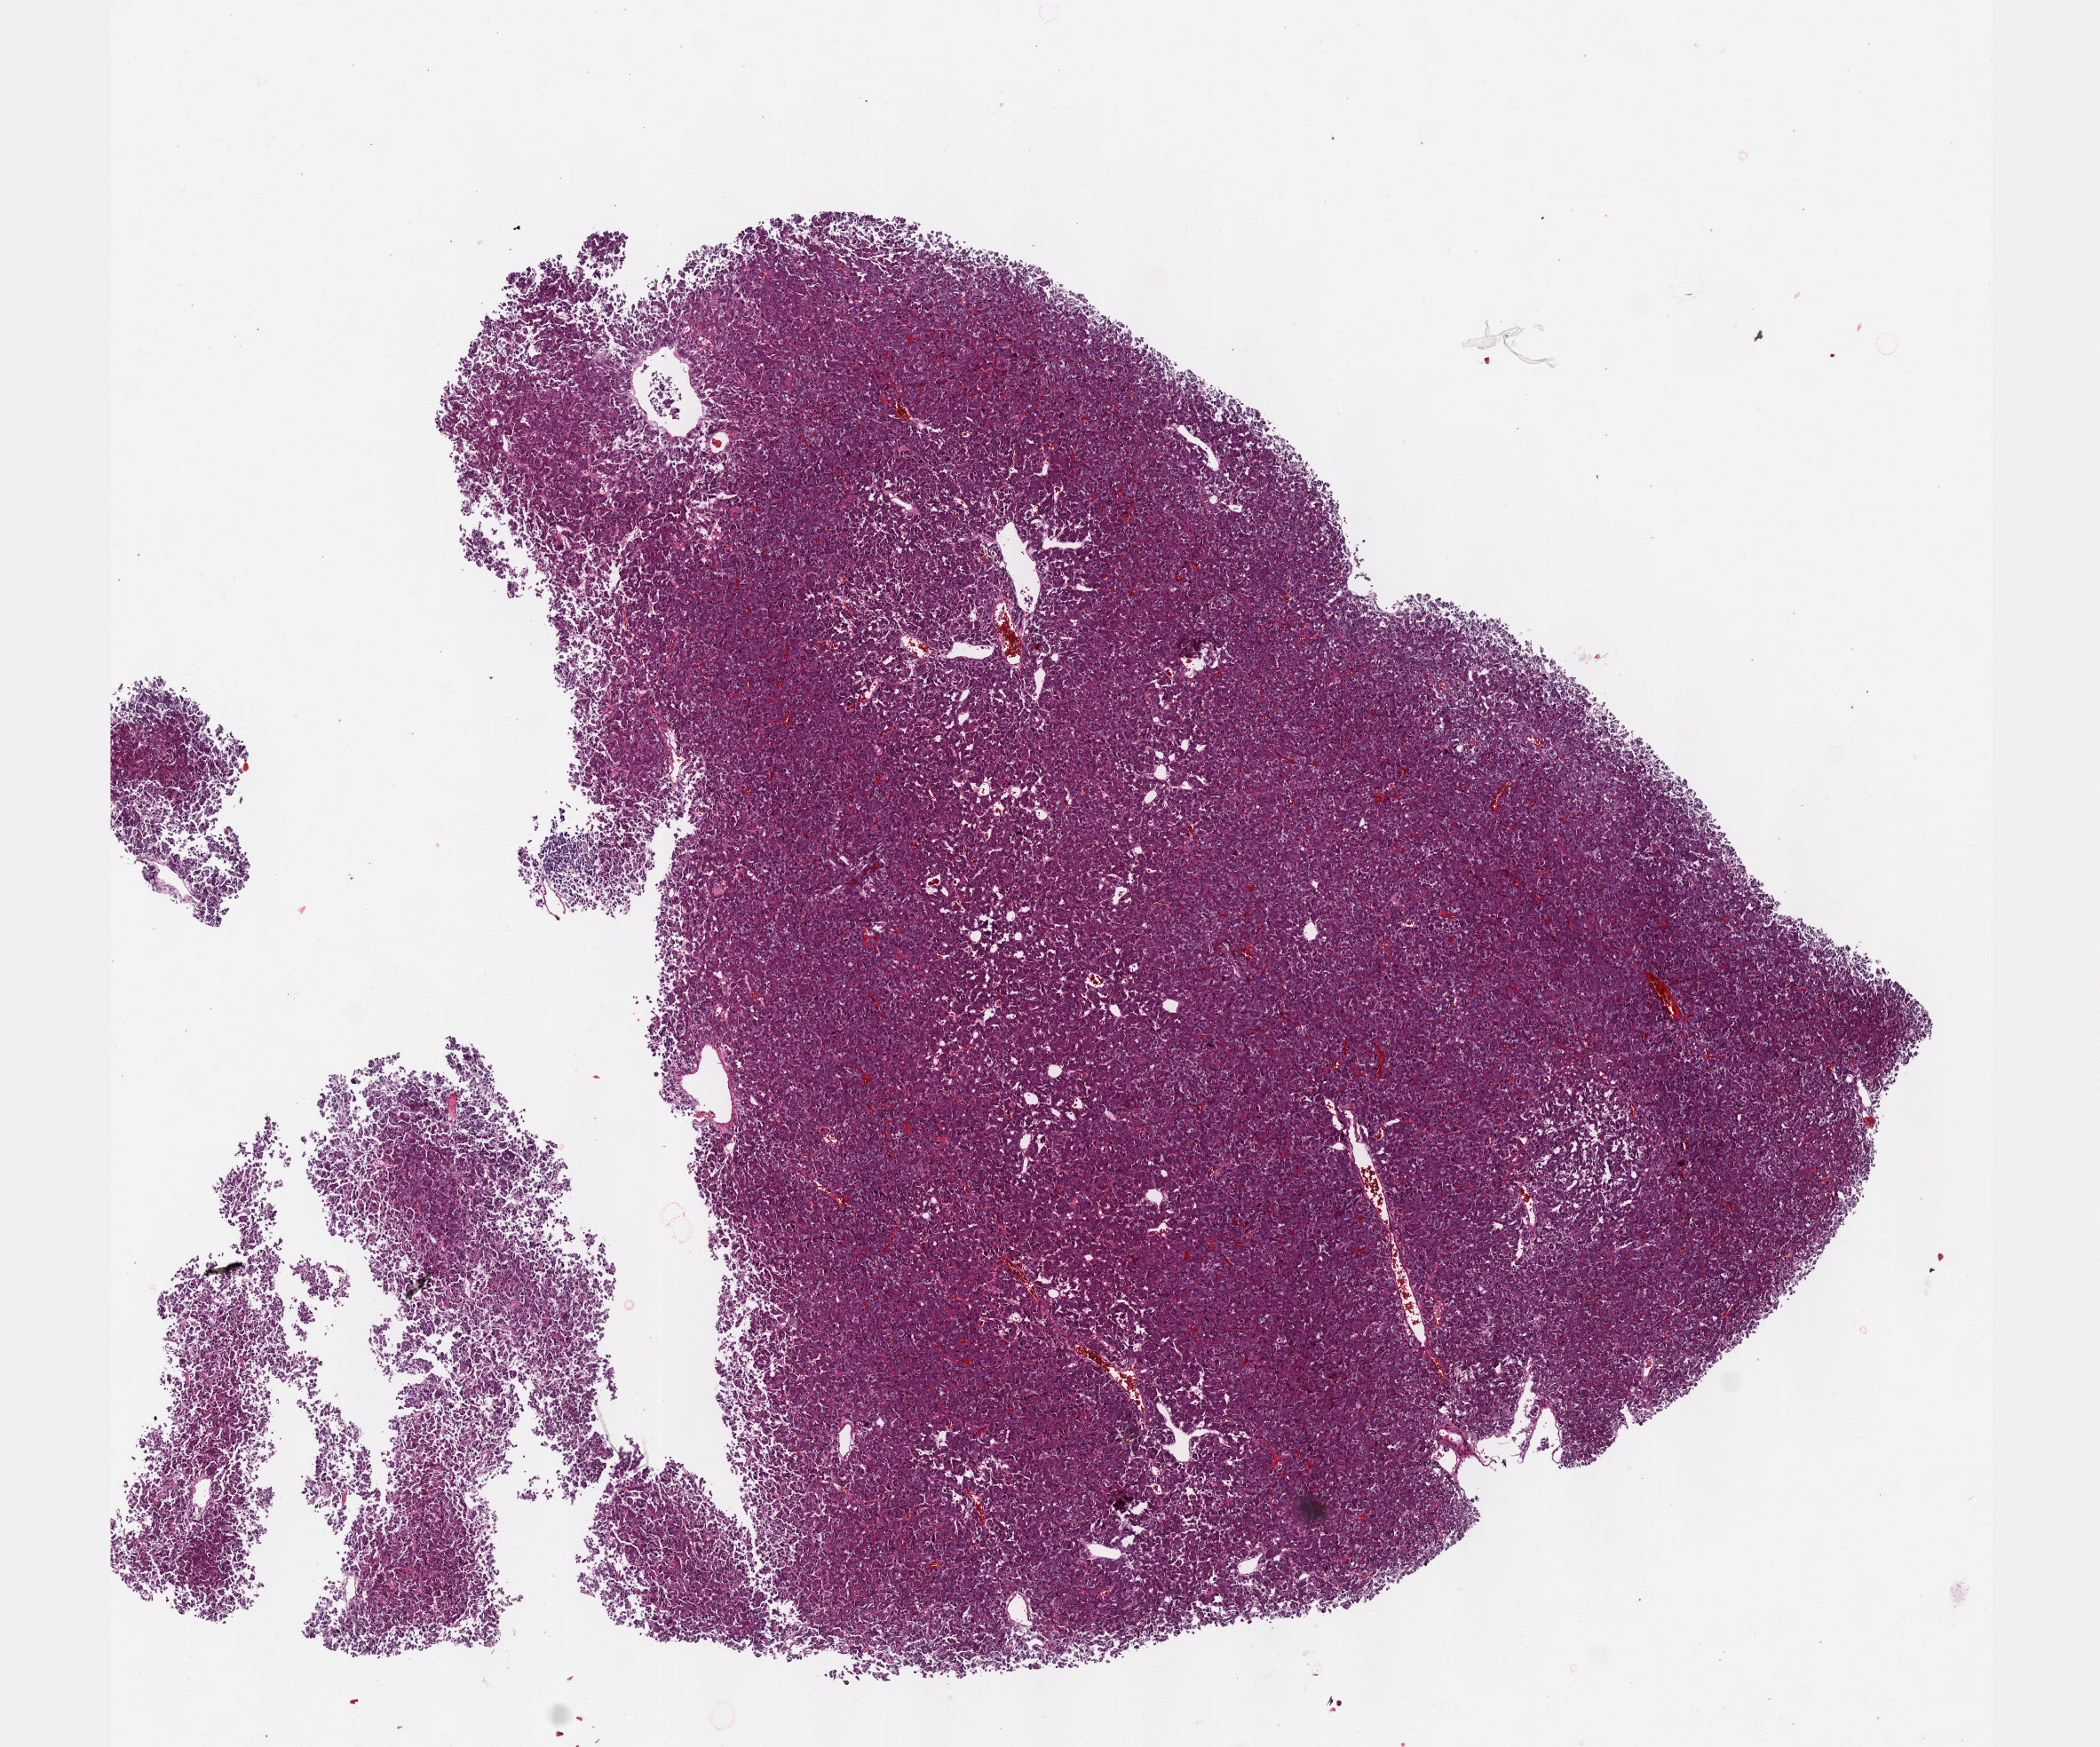
Whole-slide histology image, H&E-stained, low-resolution overview of the scanned area, about 9.6 x 8.0 mm. Formalin-fixed paraffin-embedded (FFPE) diagnostic section. Primary tumour sample from the adrenal gland. Female patient; age at initial diagnosis 55 years.
- diagnosis: Pheochromocytoma, NOS